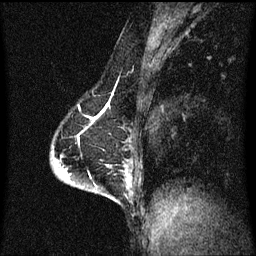
Breast MRI (dynamic contrast-enhanced), one sagittal slice; slice 34 of 60 in the series (ordered by position); dynamic contrast-enhanced series, image 2 of 3 at this slice position (ordered by acquisition); 1.5 T; TE 4.2 ms, TR 8.4 ms; 256 × 256 image matrix, field of view 200 × 200 mm. Patient: female, 64 years.
Outlined on this slice (semi-automatic segmentation, software-assisted and operator-edited):
- analysis volume of interest (the breast-tissue region the enhancement analysis was run in; not a lesion): bounding box [x1, y1, x2, y2] px = [90, 164, 129, 203]
- tumour enhancement mask (voxels above the 70 % enhancement threshold inside the analysis volume of interest): [128, 174, 129, 179]